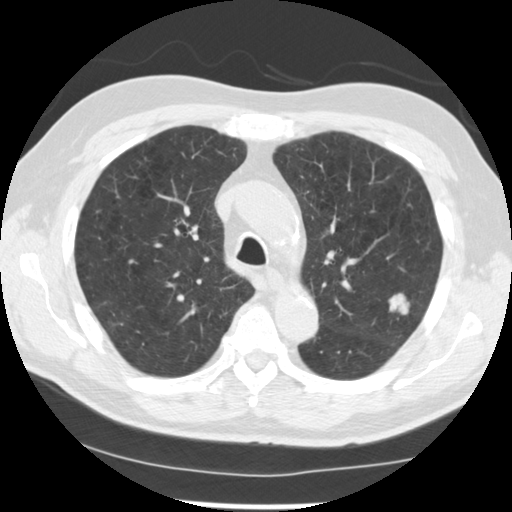
Low-dose screening chest CT, axial slice. Baseline screening round. Lung window (W 1500 / L -600 HU). 2.5 mm slice thickness. 120 kVp. Male, age 71 years at enrolment. Current smoker at enrolment.
Lesion marked by an expert reader, box from (x=377, y=283) to (x=425, y=330) px. The screening reader recorded 2 non-calcified nodules or masses ≥4 mm on this exam (left upper lobe, left upper lobe); which of them this box marks is not recorded. Official screen result: positive, change unspecified: nodule(s) >= 4 mm or enlarging nodule(s), mass(es), or other non-specific abnormalities suspicious for lung cancer. Later outcome: lung cancer diagnosed 37 days after this screen — adenocarcinoma, NOS, left upper lobe, poorly differentiated (G3), stage IIIB (AJCC 6th edition), 25 mm at pathology.